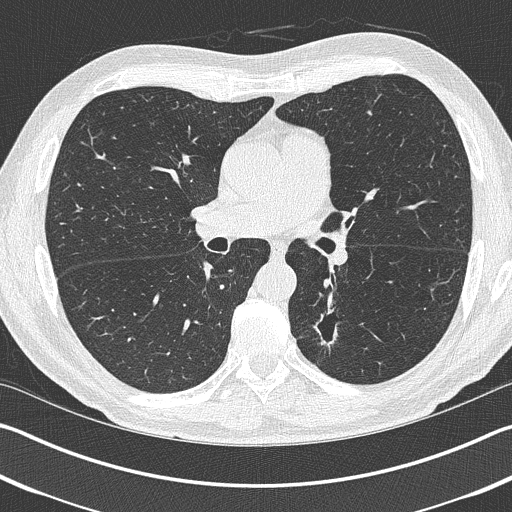
Axial slice from a low-dose chest CT screening exam, baseline annual screen, lung window (W 1500 / L -600 HU), 1 mm slice thickness, slice 169 of 402 in the series. Male, age 69 years at enrolment. Current smoker at enrolment.
Expert reader's lesion annotation, box from (x=297, y=306) to (x=353, y=362) px. The exam's reader record, not a measurement of the box and not confirmed to be the same lesion: non-calcified nodule or mass ≥4 mm, left upper lobe, 19 × 19 mm, spiculated (stellate) margins, pre-existing on the prior screen: yes. Official screen result: positive, change unspecified: nodule(s) >= 4 mm or enlarging nodule(s), mass(es), or other non-specific abnormalities suspicious for lung cancer.